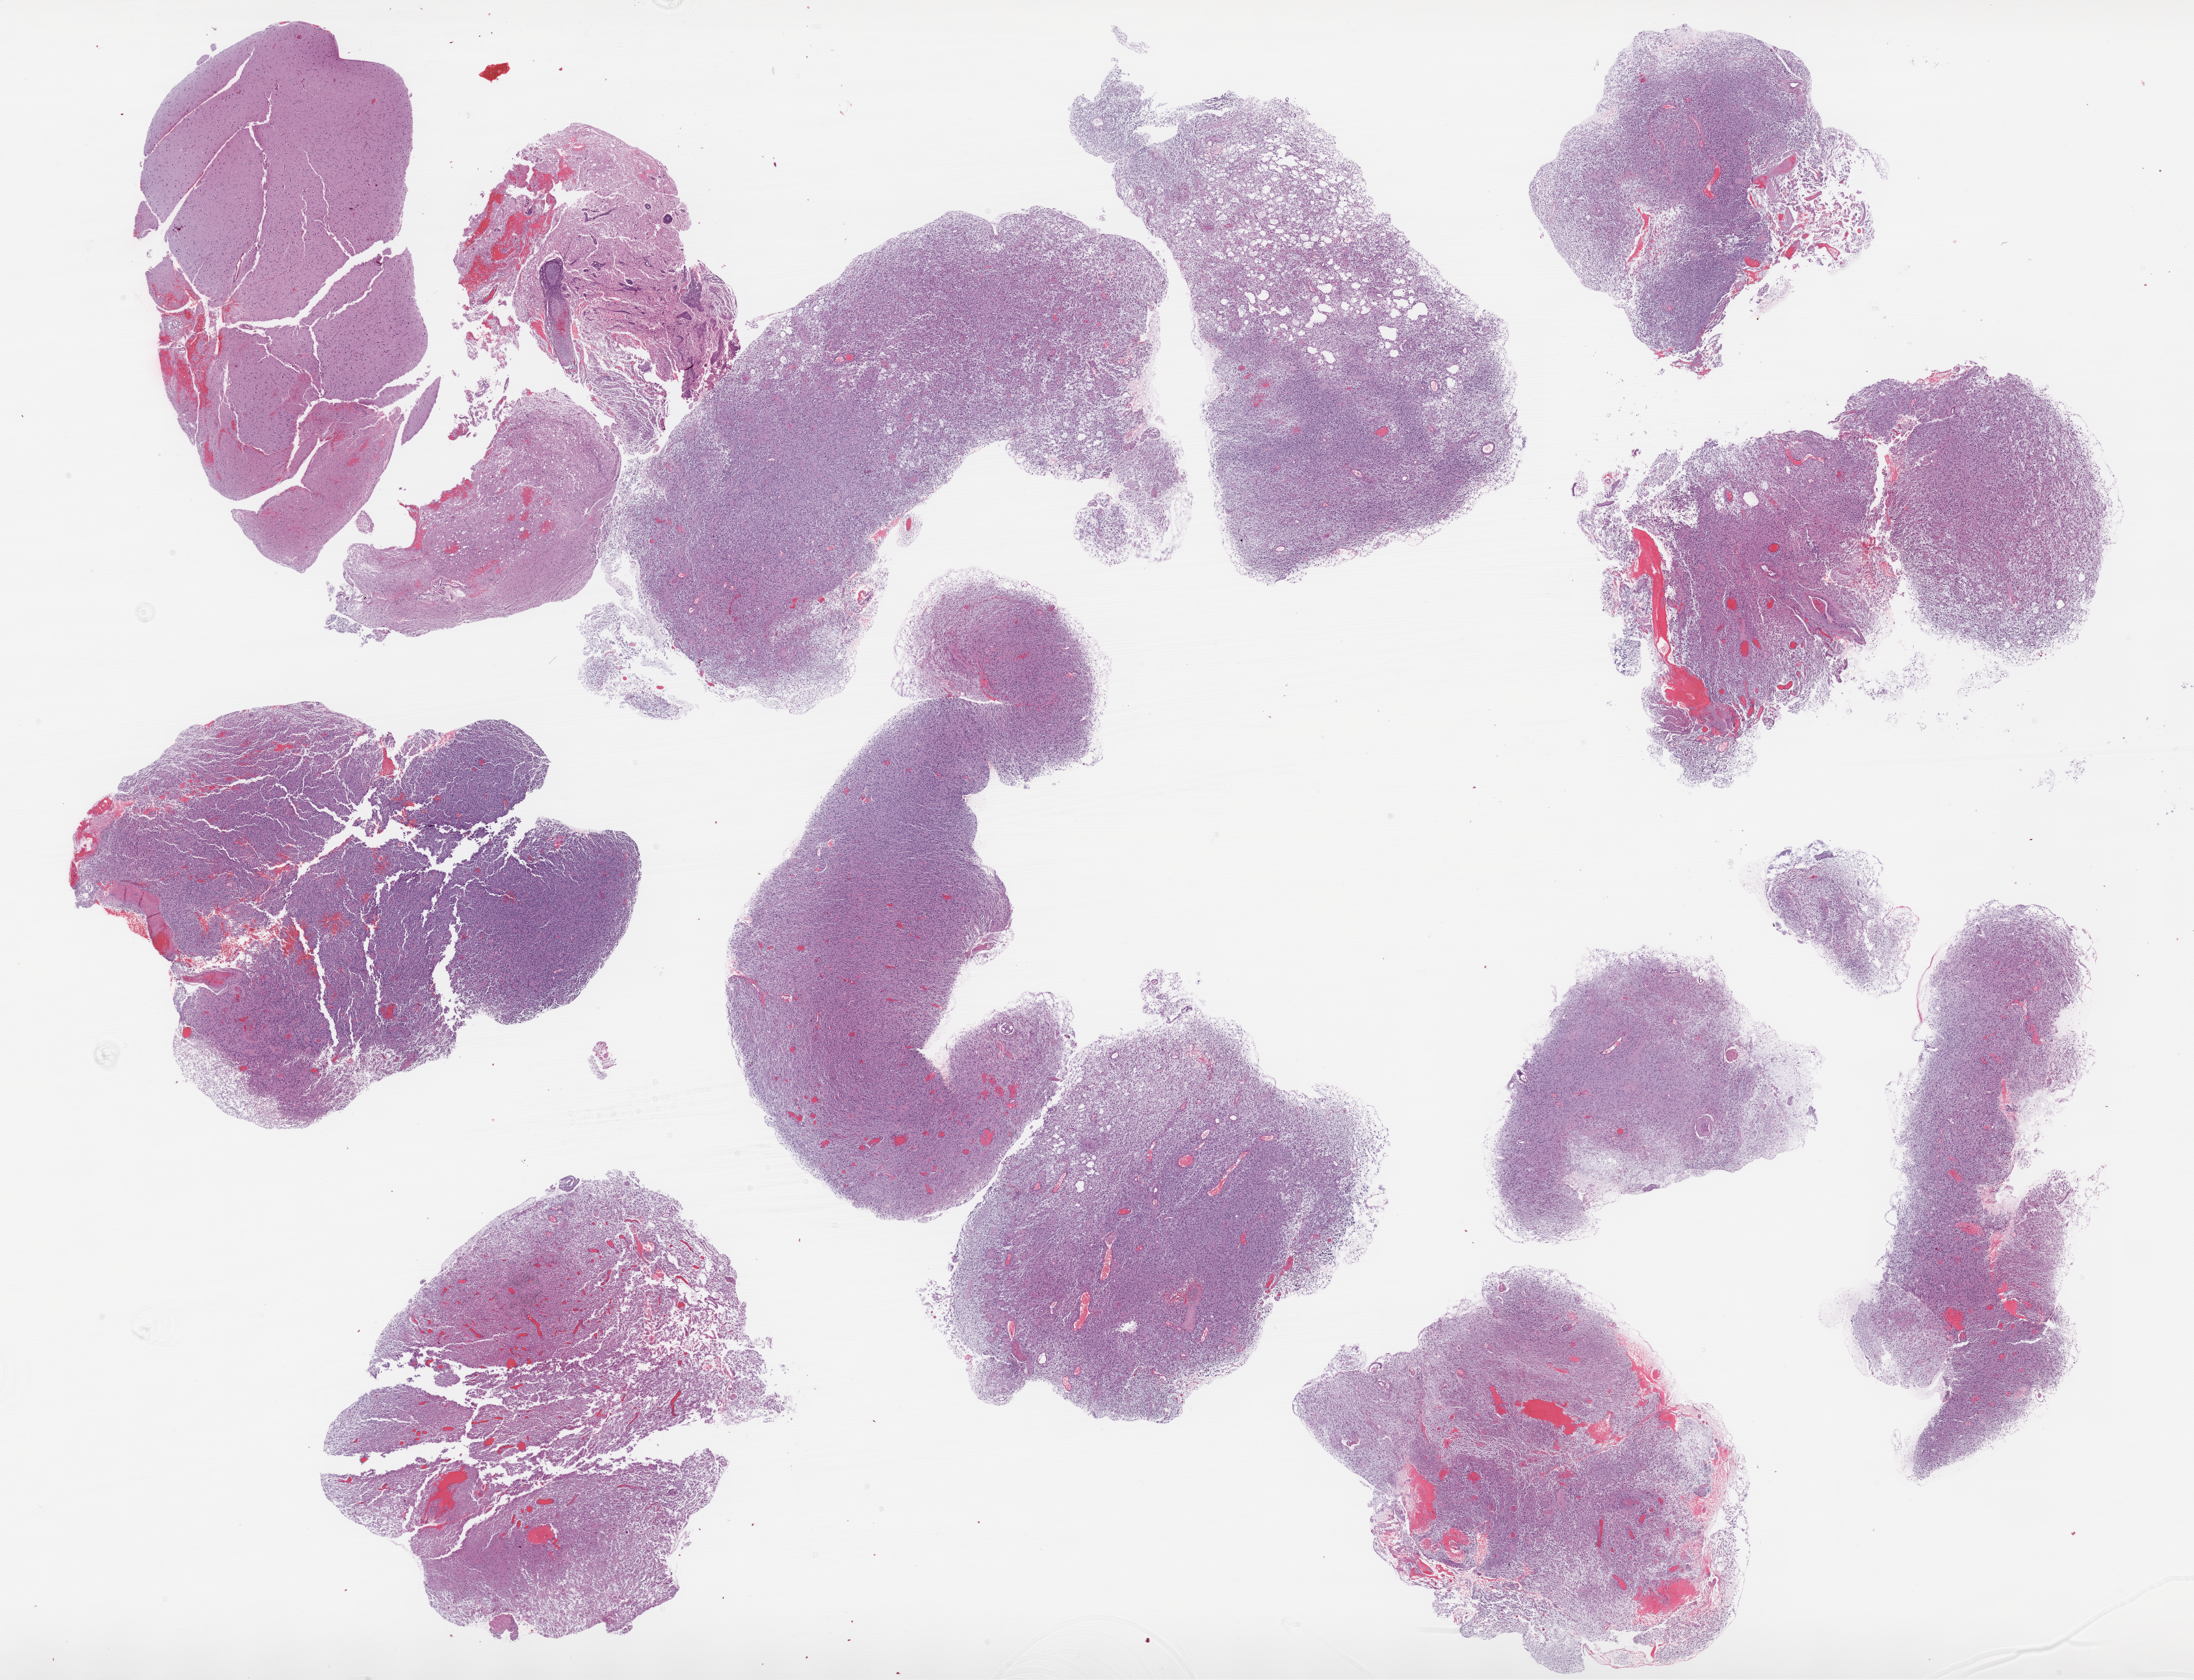
Digitized Hematoxylin and eosin (H&E) stained tissue section (whole slide), low-resolution overview of the scanned area, about 27.1 x 20.7 mm. FFPE section. Brain, primary tumour sample. Male, age 57 years at initial diagnosis.
- pathologic diagnosis: Glioblastoma